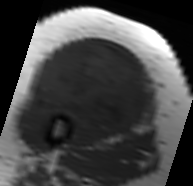
MRI of an extremity soft-tissue mass, one axial slice. Position 37 of 91 along the scan axis. MR volume resampled by the dataset authors to the PET/CT grid (not the native acquisition matrix). 3.27 mm slice thickness. 193 × 186 image matrix. Female patient. Case-level facts recorded for this patient, not image findings: histological type: malignant solitary fibrous tumor; grade: intermediate; site of the primary tumour: right thigh.
Structures marked on this image (expert contour drawn on MRI and transferred to this co-registered scan by the dataset authors):
- gross tumour volume including surrounding oedema: bounding box (x1, y1, x2, y2) in pixels: (28, 40, 153, 136)
- gross tumour volume (mass): (33, 42, 148, 132)